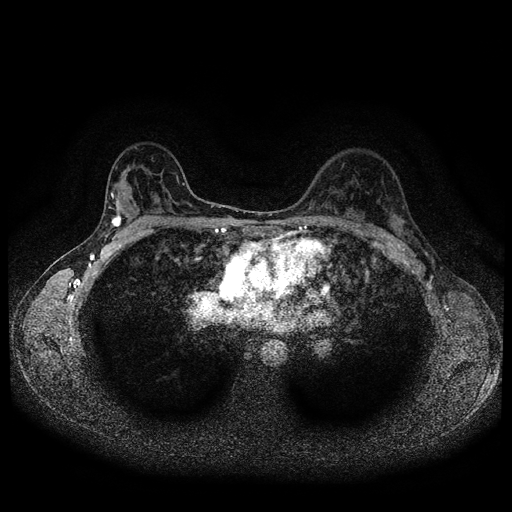
Breast MRI (dynamic contrast-enhanced, multi-phase), one axial slice. Position 65 of 116 along the scan axis. Dynamic contrast-enhanced series, time point 2 of 5 at this slice position (early post-contrast). 1.5 T. TE 2.7 ms, TR 5.4 ms. 2 mm slice thickness. 512 × 512 image matrix, field of view 330 × 330 mm. Female patient, age 36 years.
Outlined on this slice (semi-automatically segmented with operator editing):
- breast lesion (labelled 'tumour' in the annotation; benign lesions carry a separate 'benign' label): bounding box [x1, y1, x2, y2] px = [111, 212, 123, 229]